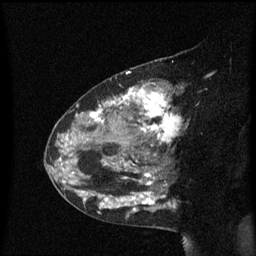
Breast MRI (dynamic contrast-enhanced), one sagittal slice; dynamic contrast-enhanced series, image 2 of 3 at this slice position (ordered by acquisition); 1.5 T; TE 4.2 ms, TR 8.4 ms; 2 mm slice thickness; 256 × 256 image matrix. Patient: female, 48 years. Case-level facts recorded for this patient, not image findings: setting: breast cancer imaged before/during neoadjuvant chemotherapy; receptor status: HR-positive, HER2-negative.
Annotated regions visible in this slice (semi-automatically segmented with operator editing):
- analysis volume of interest (the breast-tissue region the enhancement analysis was run in; not a lesion): box from (x=80, y=81) to (x=187, y=220) px
- tumour enhancement mask (voxels above the 70 % enhancement threshold inside the analysis volume of interest): (x=80, y=84)–(x=183, y=213)